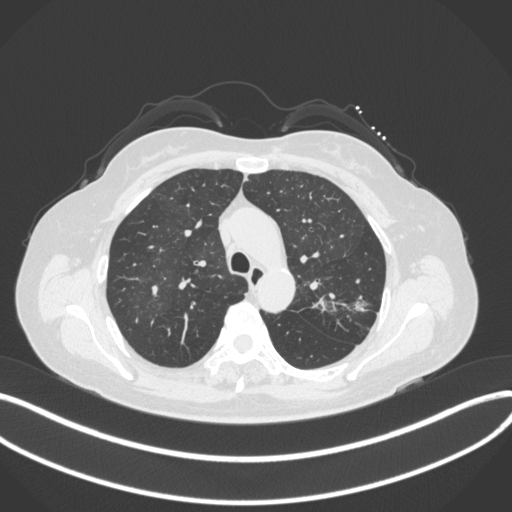
Chest CT, one axial slice. Position 248 of 330 along the scan axis. 120 kVp. Lung window (W 1500 / L -600 HU). 1 mm slice thickness. 512 × 512 image matrix, field of view 400 × 400 mm. Female patient, age 60 years. Case-level facts recorded for this patient, not image findings: clinical TNM (as recorded): T1c N0 M0.
Annotated regions visible in this slice (bounding box drawn by a radiologist):
- lung tumour (recorded histology: adenocarcinoma): bounding box (x1, y1, x2, y2) in pixels: (349, 292, 372, 317)